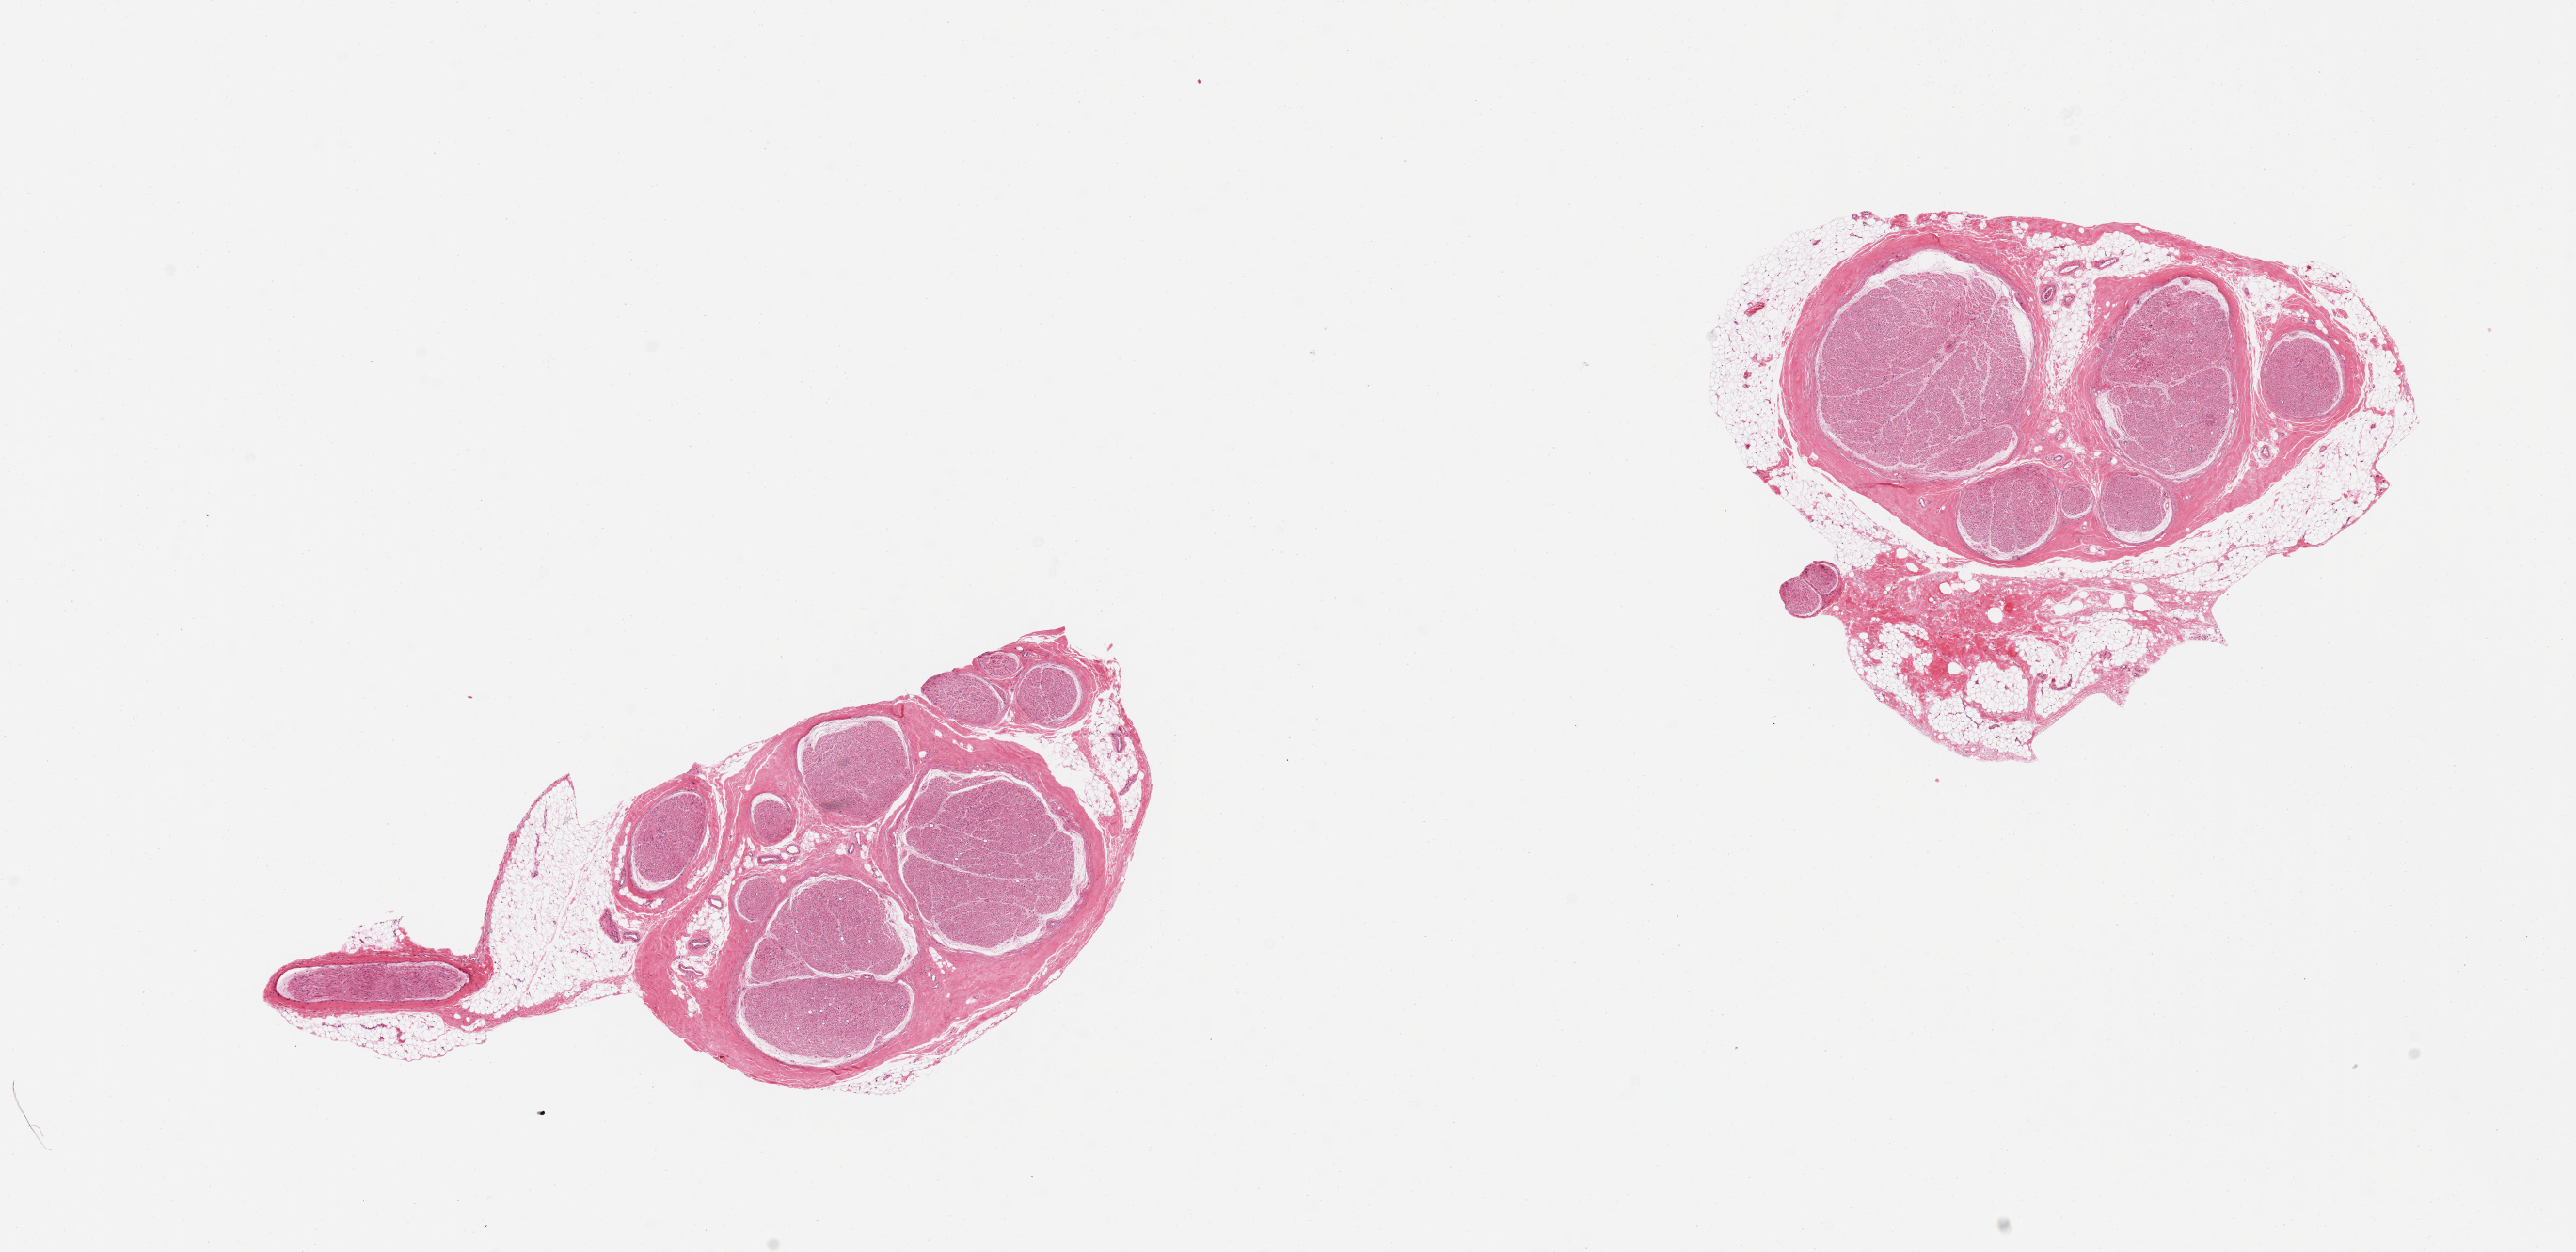
Haematoxylin and eosin whole-slide image, brightfield, whole scanned area (about 21.7 x 10.5 mm, from a 20x scan) shown as a low-resolution overview, PAXgene-fixed paraffin-embedded (PFPE) section, target tissue: tibial nerve, donor tissue sample. Donor sex: male.
Pathologist's review note for this sample: 2 pieces, one has attached fat ~20%, second has partial rim of fat up to 40%.